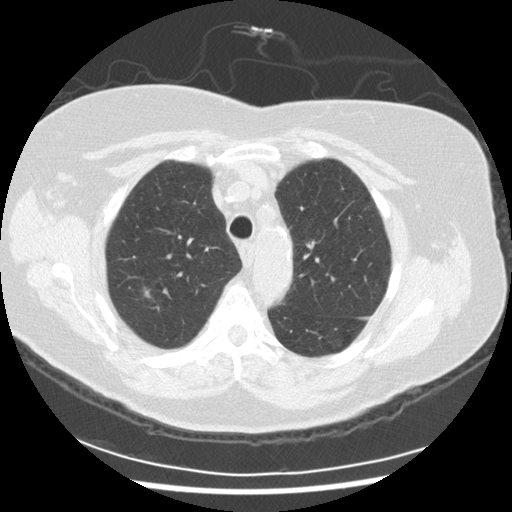
Axial slice from a low-dose chest CT screening exam, third screening round (two years after baseline), lung window (W 1500 / L -600 HU), 2.5 mm slice thickness, standard (soft-tissue) reconstruction kernel (STANDARD), slice 51 of 254 in the series, 512 × 512 image matrix. Female participant, aged 72 years at enrolment. Current smoker at enrolment.
Expert-annotated lung lesion, bounding box <126,280,159,308> (left, top, right, bottom; pixels). The exam's reader record, not a measurement of the box and not confirmed to be the same lesion: non-calcified nodule or mass ≥4 mm, right upper lobe, 9 × 8 mm, poorly defined margins, ground glass attenuation, pre-existing on the prior screen: no. Lung cancer was diagnosed 121 days after this screen: squamous cell carcinoma, NOS, right upper lobe, poorly differentiated (G3), stage IIIA (AJCC 6th edition), 22 mm at pathology.